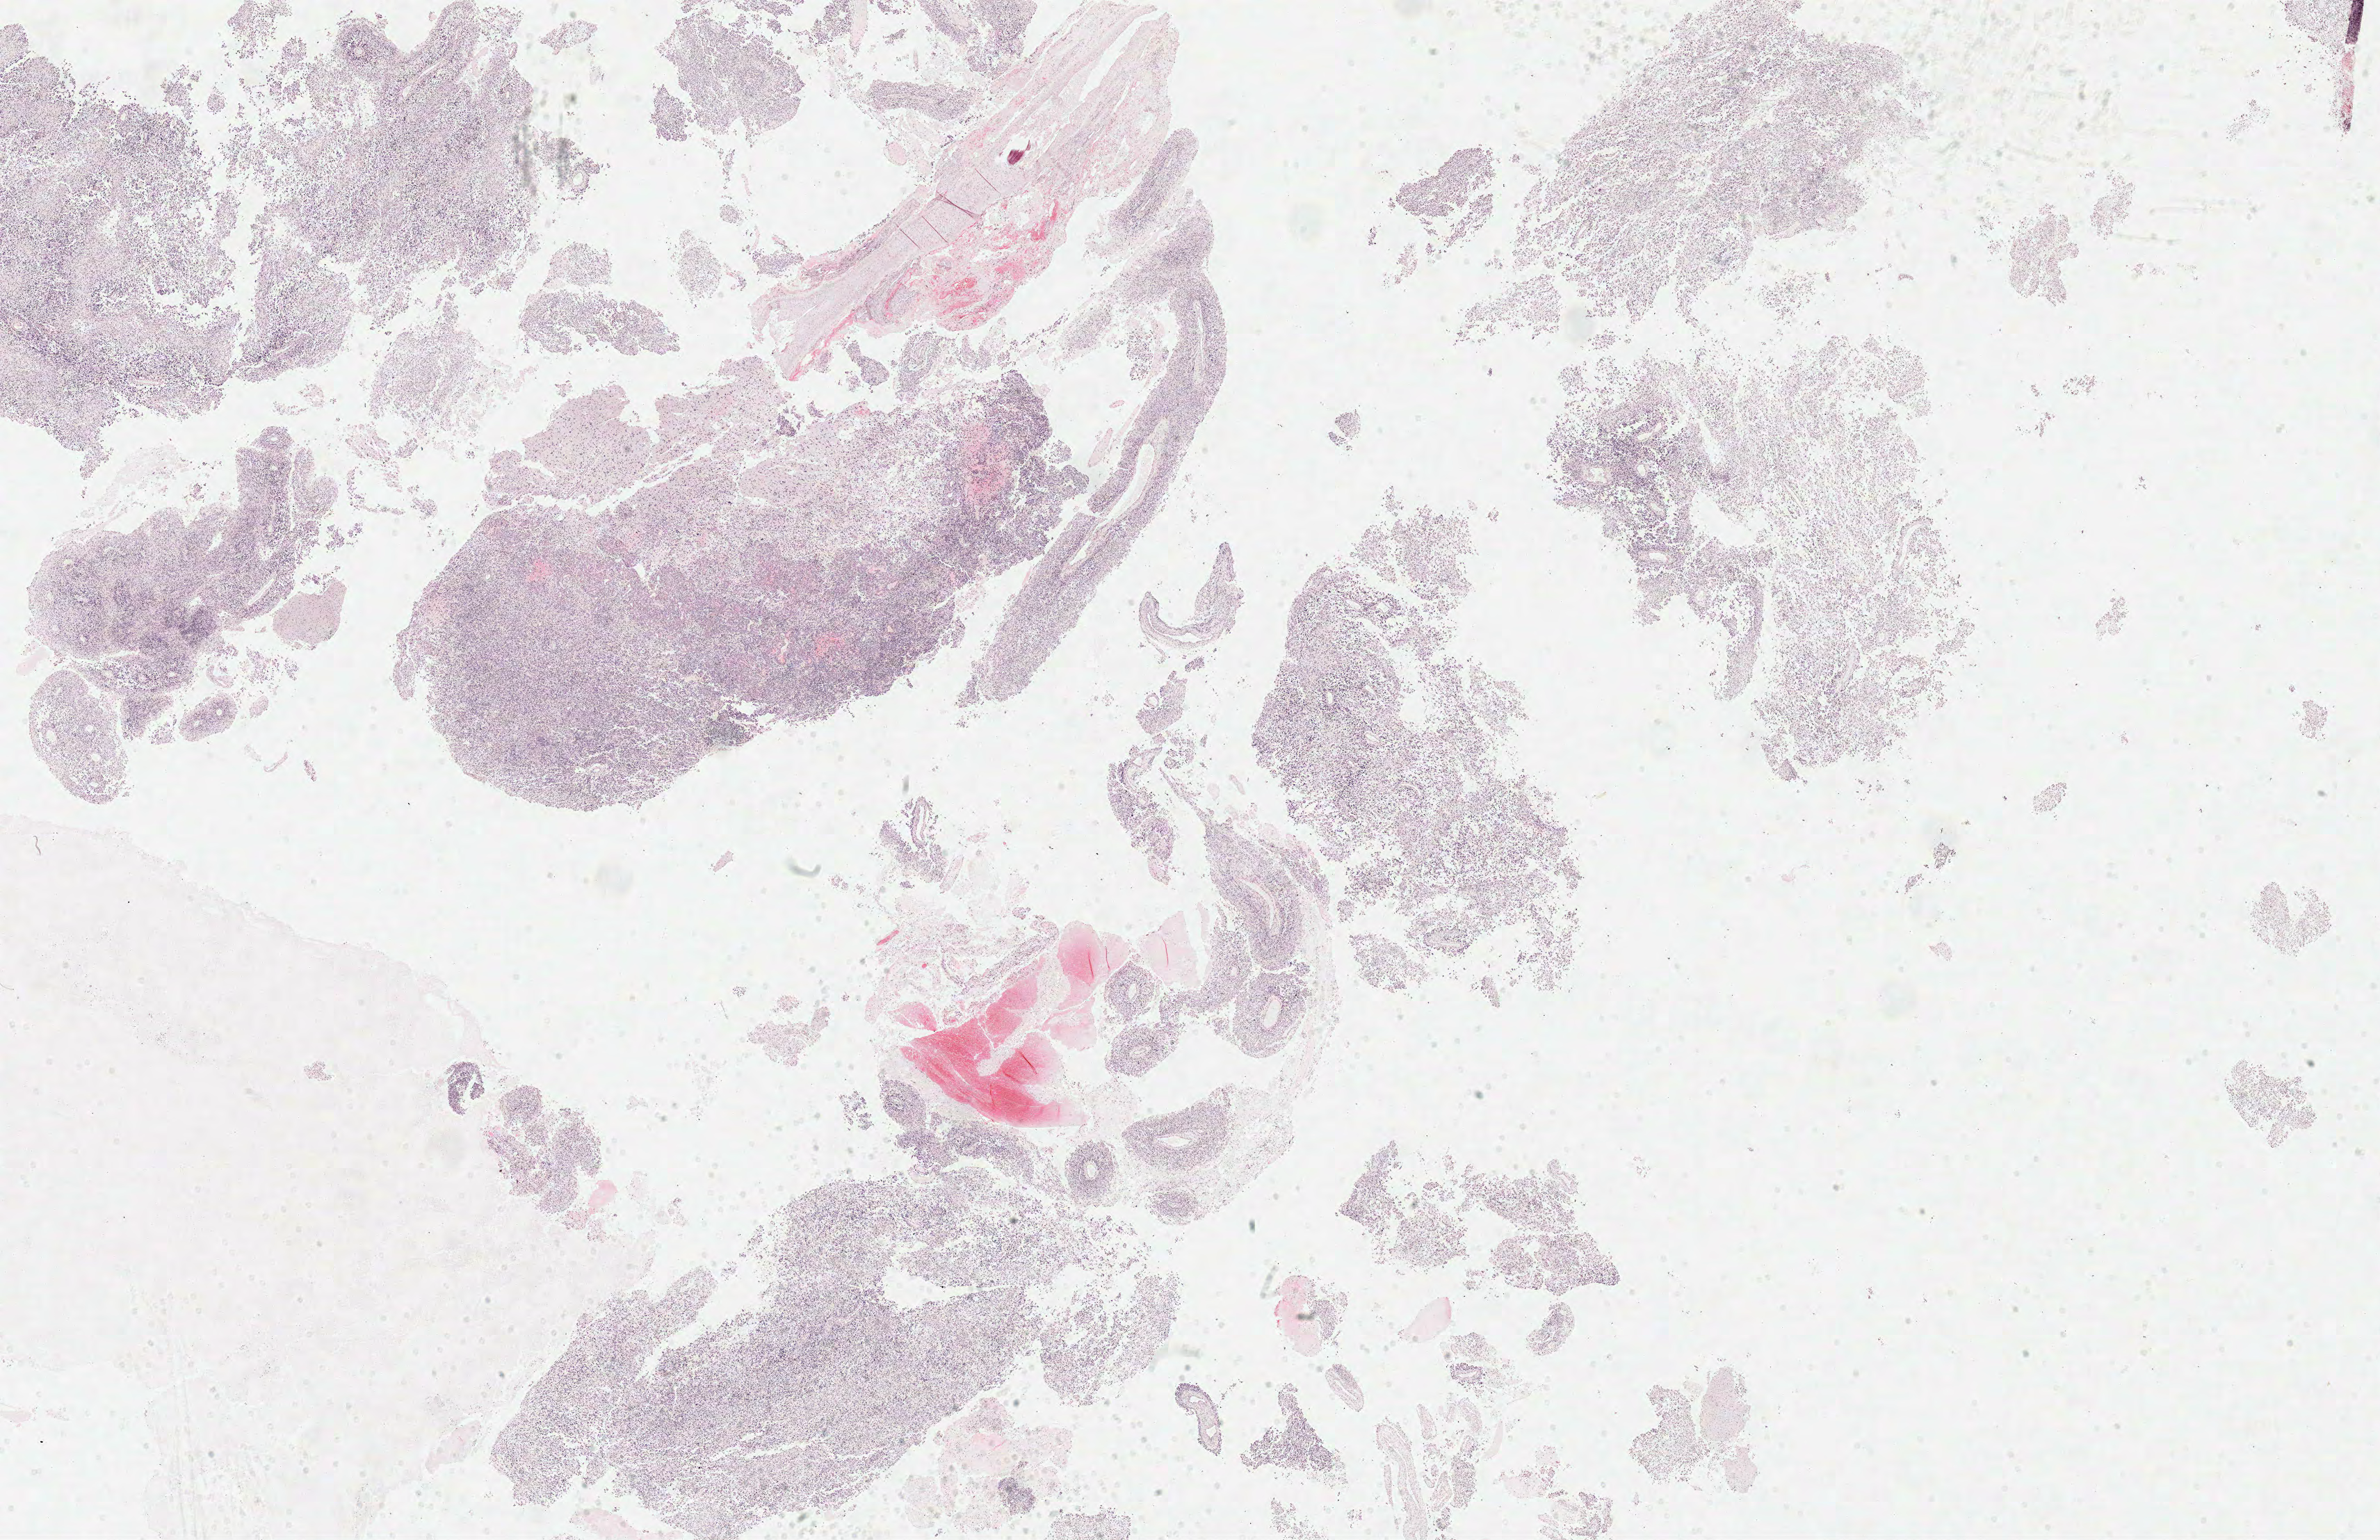
Whole-slide histology image, H&E — whole scanned area (about 26.9 x 17.4 mm, slide scanned at 40x) shown as a low-resolution overview. Formalin-fixed paraffin-embedded (FFPE) diagnostic section. Brain, primary tumour sample. Patient: female, age at initial diagnosis 72 years.
- pathologic diagnosis: Glioblastoma